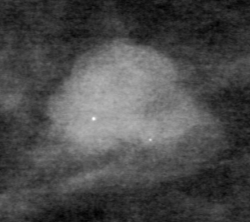
Cropped region of a digitized screen-film mammogram centred on a radiologist-marked abnormality, right breast, CC view, BI-RADS breast density category 2 (scale 1–4).
Mass, shape lobulated, margins circumscribed; BI-RADS assessment category 4; pathology (as recorded): malignant.